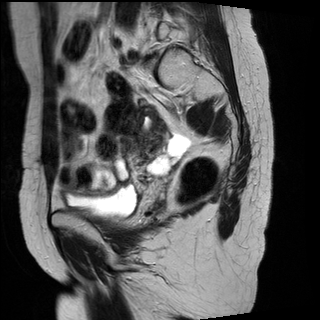
Pelvic MRI for cervical cancer, one sagittal slice. Slice 10 of 29 in the series (ordered by position). T2-weighted. 1.5 T. TE 89 ms, TR 2930 ms. 4 mm slice thickness. 320 × 320 image matrix. Patient: female, 45 years.
Outlined on this slice (outlined manually by an expert reader):
- uterus and cervix: bounding box [x1, y1, x2, y2] px = [125, 105, 167, 160]